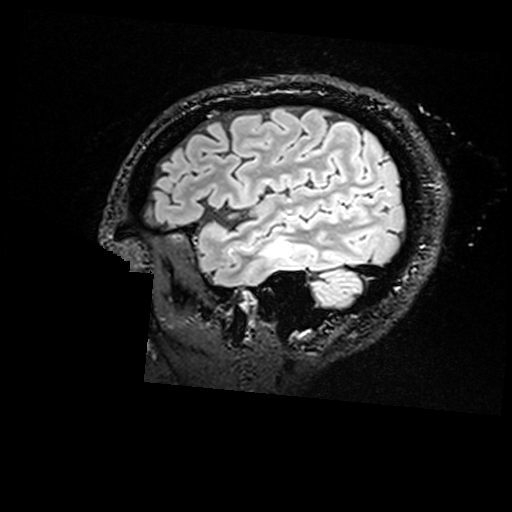
Brain MRI from a brain-tumour surgery series, one sagittal slice. Slice 131 of 176 in the series (ordered by position). T2 FLAIR. 1 mm slice thickness. 512 × 512 image matrix, field of view 250 × 250 mm. Case-level facts recorded for this patient, not image findings: histopathology: Non-tumor destructive chronic inflammatory lesion with abnormal vasculature; tumour location: Right Inferior Temporal.
Structures marked on this image (manually delineated by an expert):
- residual tumour: bounding box [x1, y1, x2, y2] px = [280, 242, 293, 256]